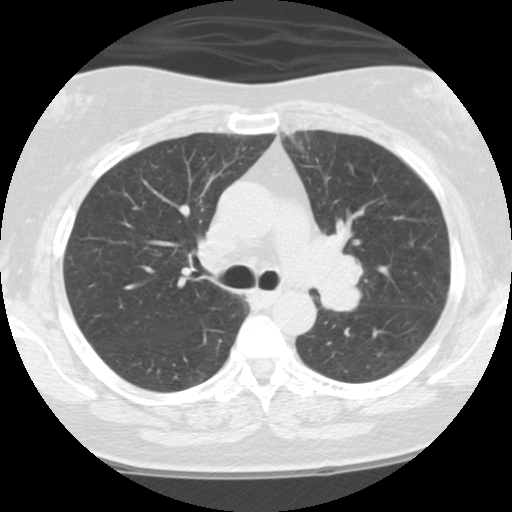
Low-dose screening chest CT, axial slice, third annual screen, lung window (W 1500 / L -600 HU), 2.5 mm slice thickness, standard (soft-tissue) reconstruction kernel (STANDARD), slice 37 of 108 in the series, 512 × 512 image matrix, field of view 300 × 300 mm. Female, age 59 years at enrolment. Current smoker at enrolment.
Expert reader's lesion annotation, bounding box <285,213,381,325> (left, top, right, bottom; pixels). No non-calcified nodule or mass ≥4 mm was recorded by the screening reader at this exam. Participant outcome: lung cancer diagnosed 192 days after this screen — small cell carcinoma, NOS, left upper lobe, left hilum, mediastinum, left main stem bronchus, stage IV (AJCC 6th edition), 63 mm at pathology.